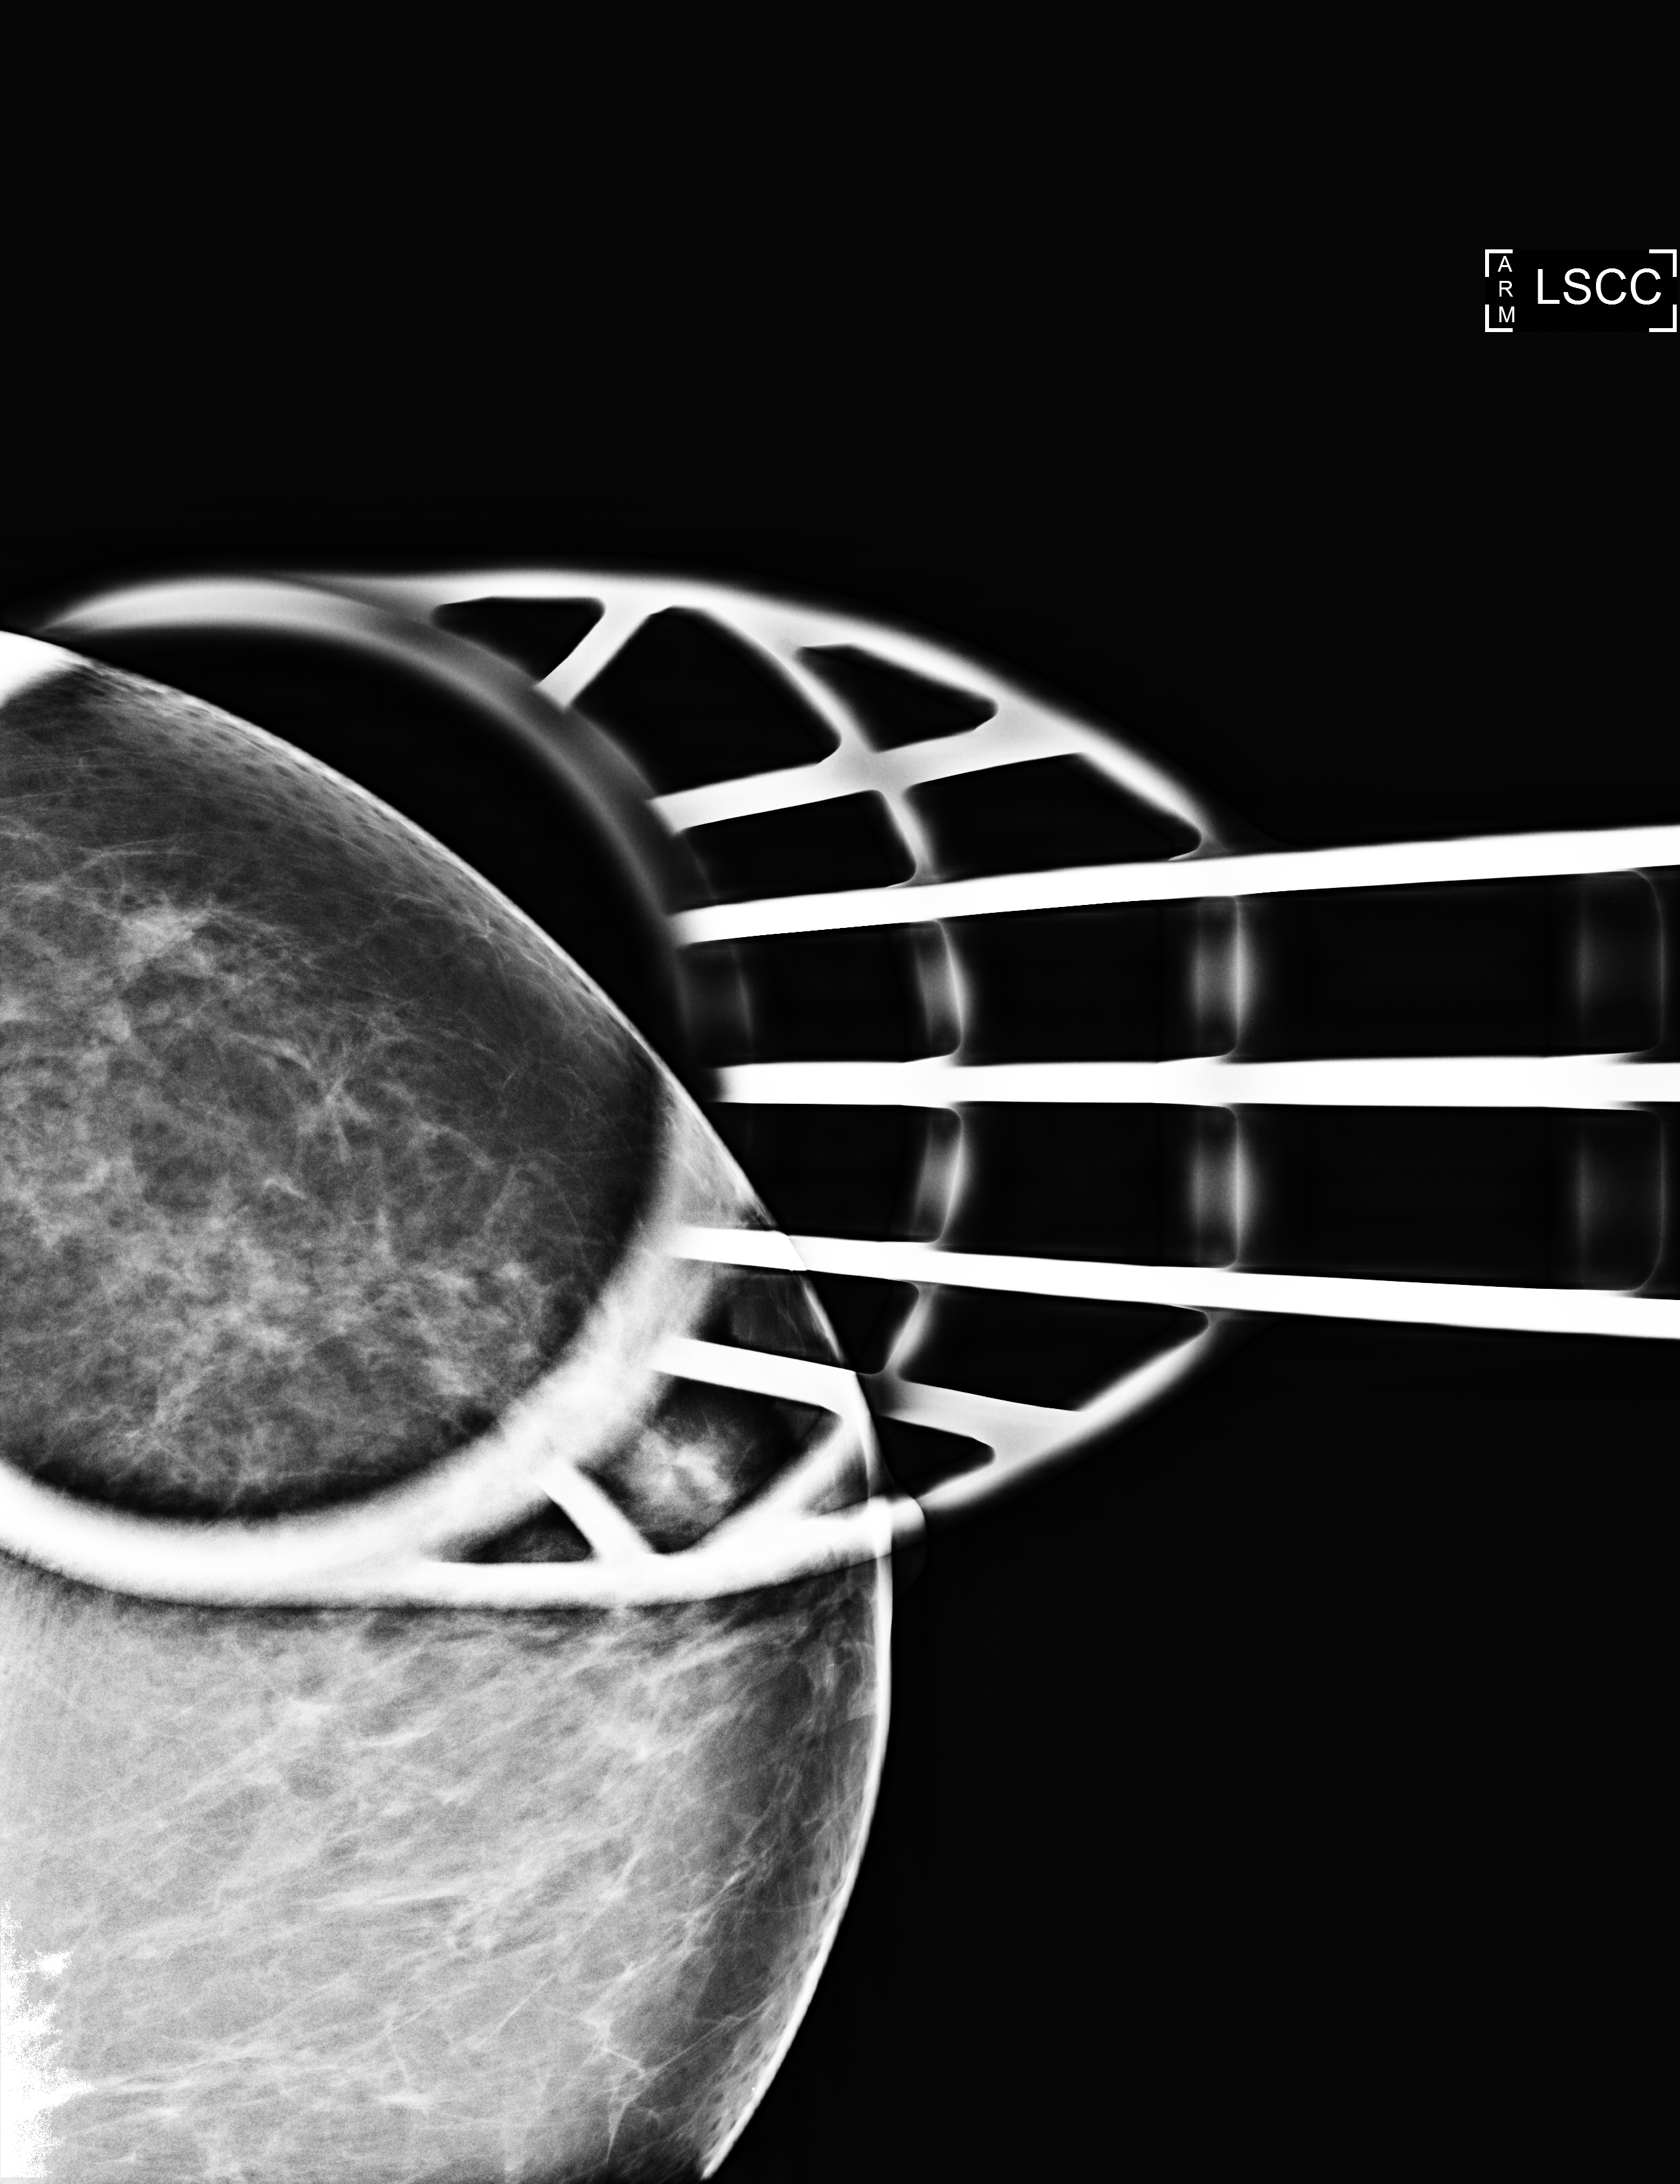
Additional (diagnostic) view, compressed breast thickness 60 mm.
Image type: full-field digital mammogram. Breast: left. Projection: cranio-caudal projection, spot compression.